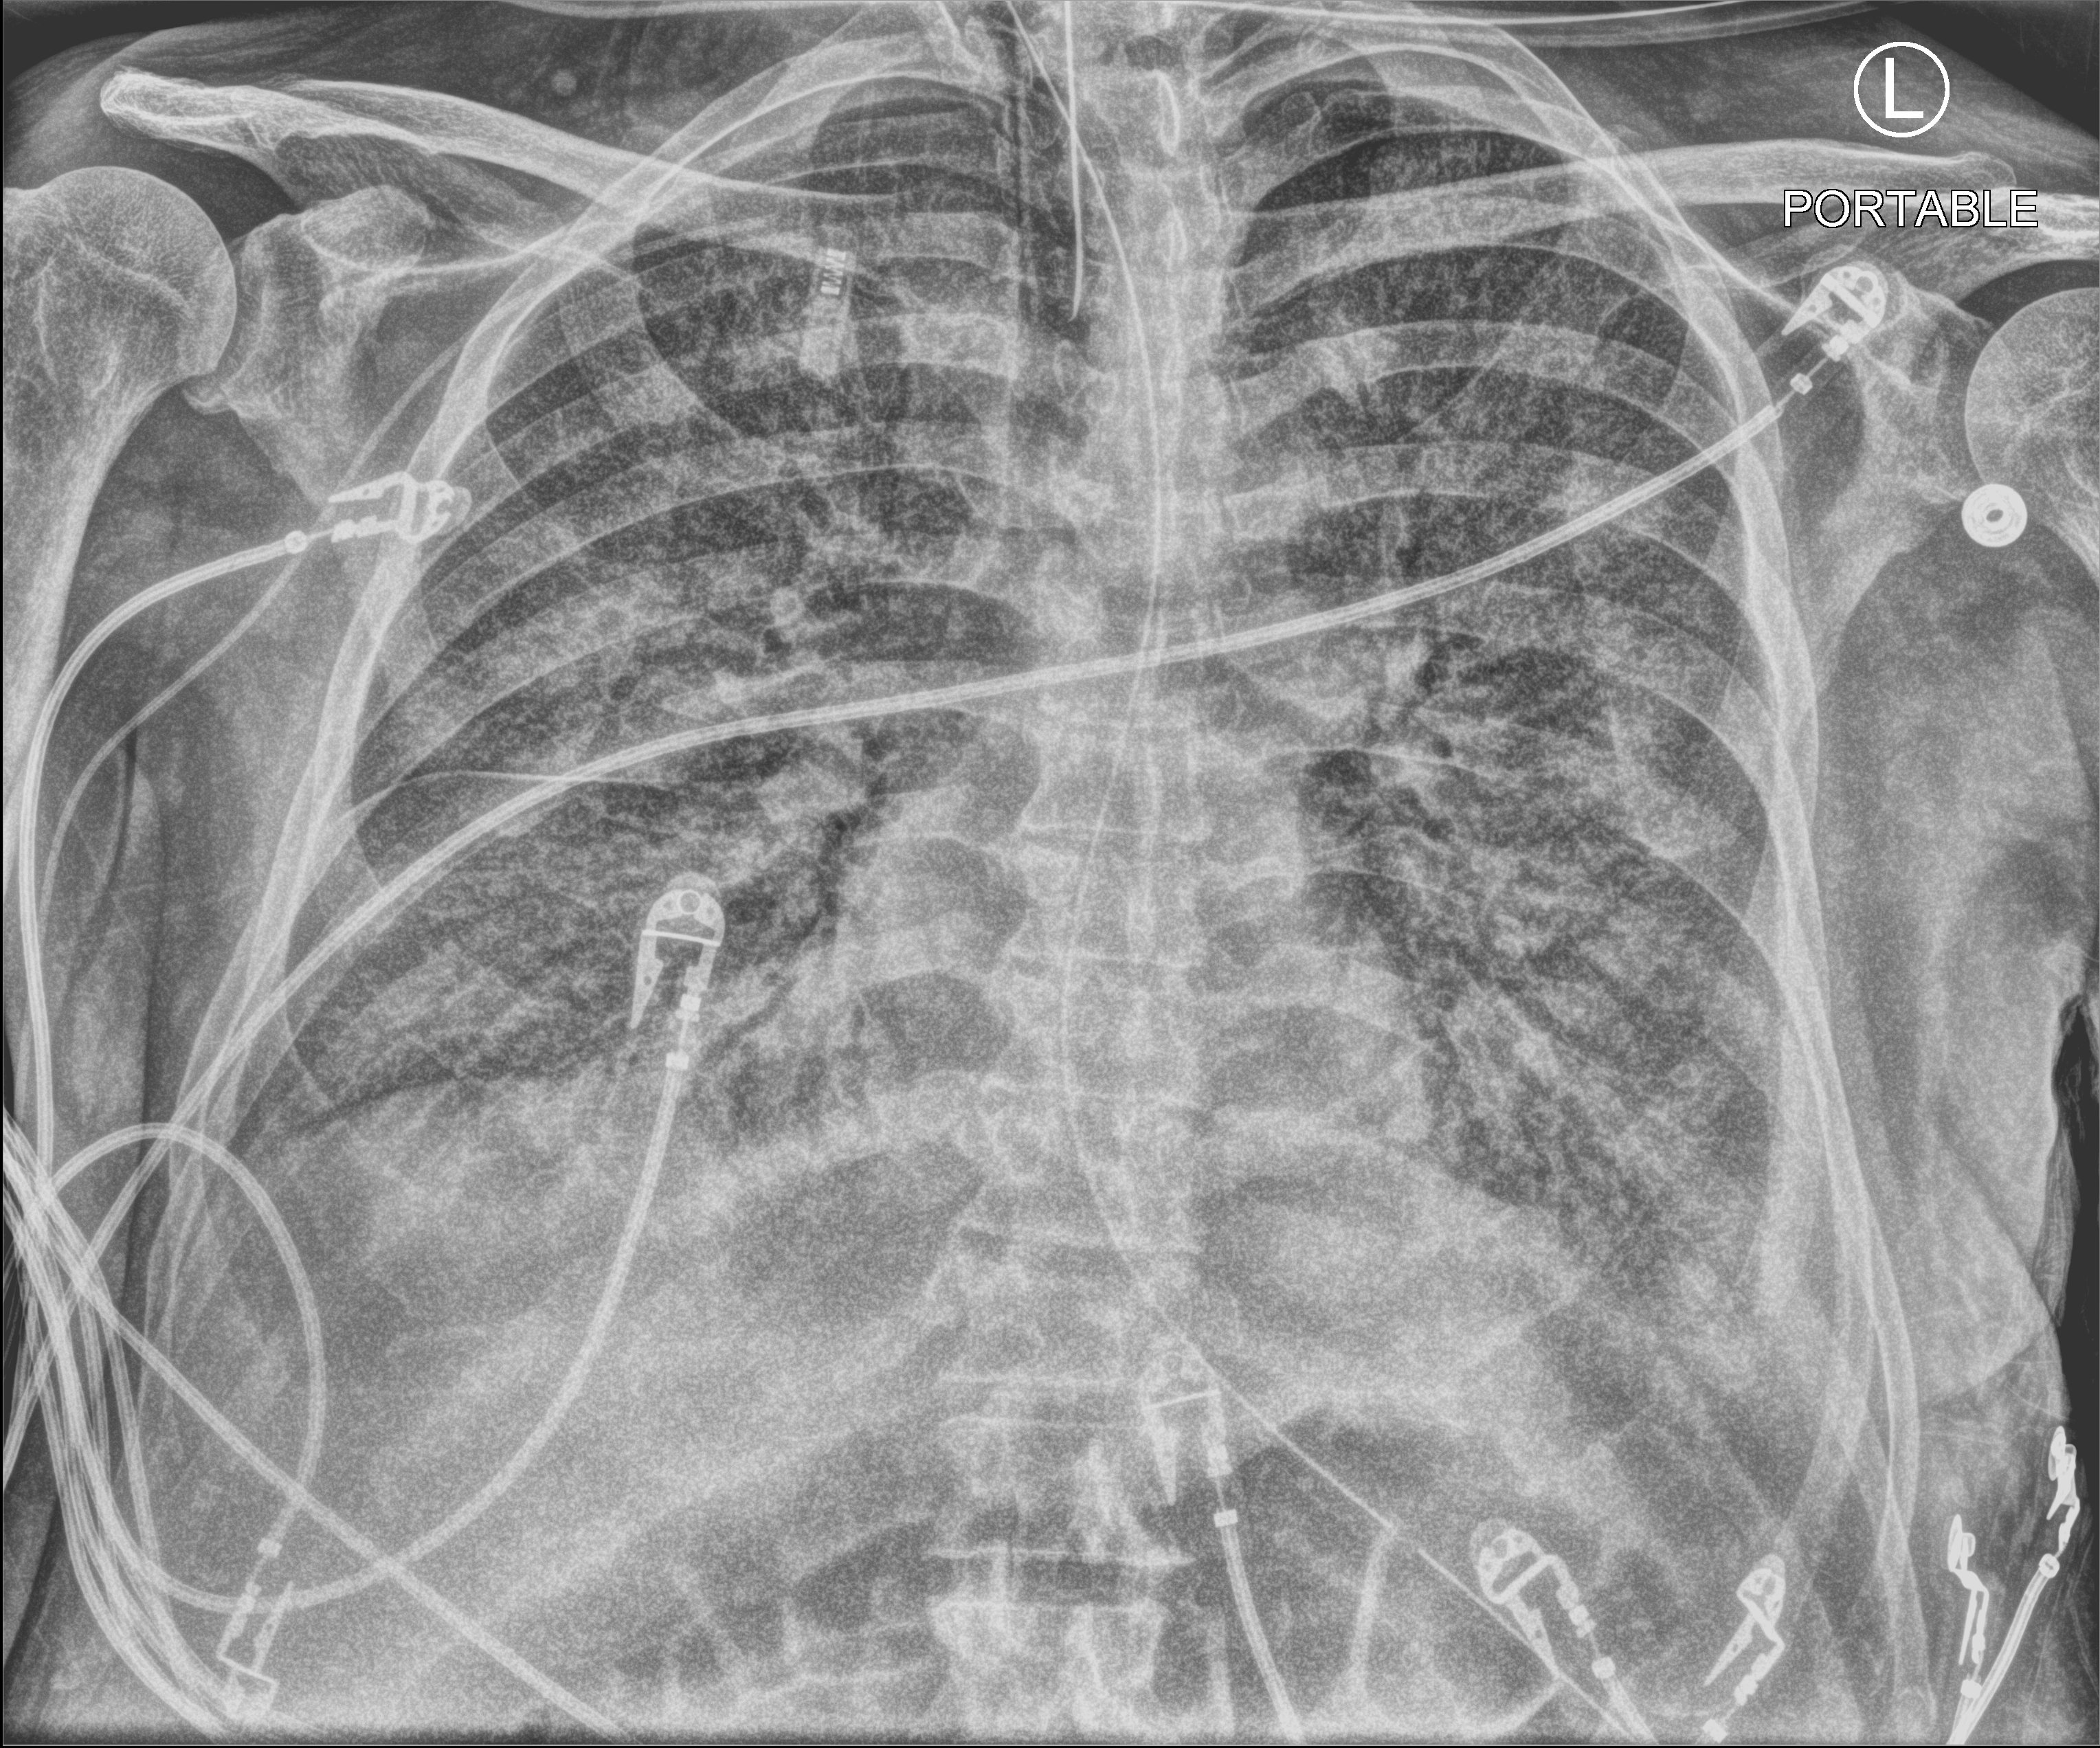
Portable chest radiograph, anteroposterior (AP) projection. Male patient hospitalised with COVID-19, age 60–74 years.
From the hospital-stay record, not from the radiograph (when in the stay this image was taken is not recorded): mechanically ventilated during this hospital stay: yes.